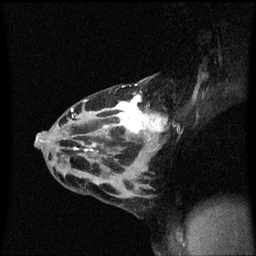
Breast MRI (dynamic contrast-enhanced), one sagittal slice; slice 35 of 60 in the series (ordered by position); dynamic contrast-enhanced series, image 2 of 3 at this slice position (ordered by acquisition); 1.5 T; TE 4.2 ms, TR 8.4 ms; 256 × 256 image matrix. Female patient, age 32 years.
Outlined on this slice (semi-automatically segmented with operator editing):
- analysis volume of interest (the breast-tissue region the enhancement analysis was run in; not a lesion): bounding box <55,78,170,167> (left, top, right, bottom; pixels)
- tumour enhancement mask (voxels above the 70 % enhancement threshold inside the analysis volume of interest): <72,94,167,153>